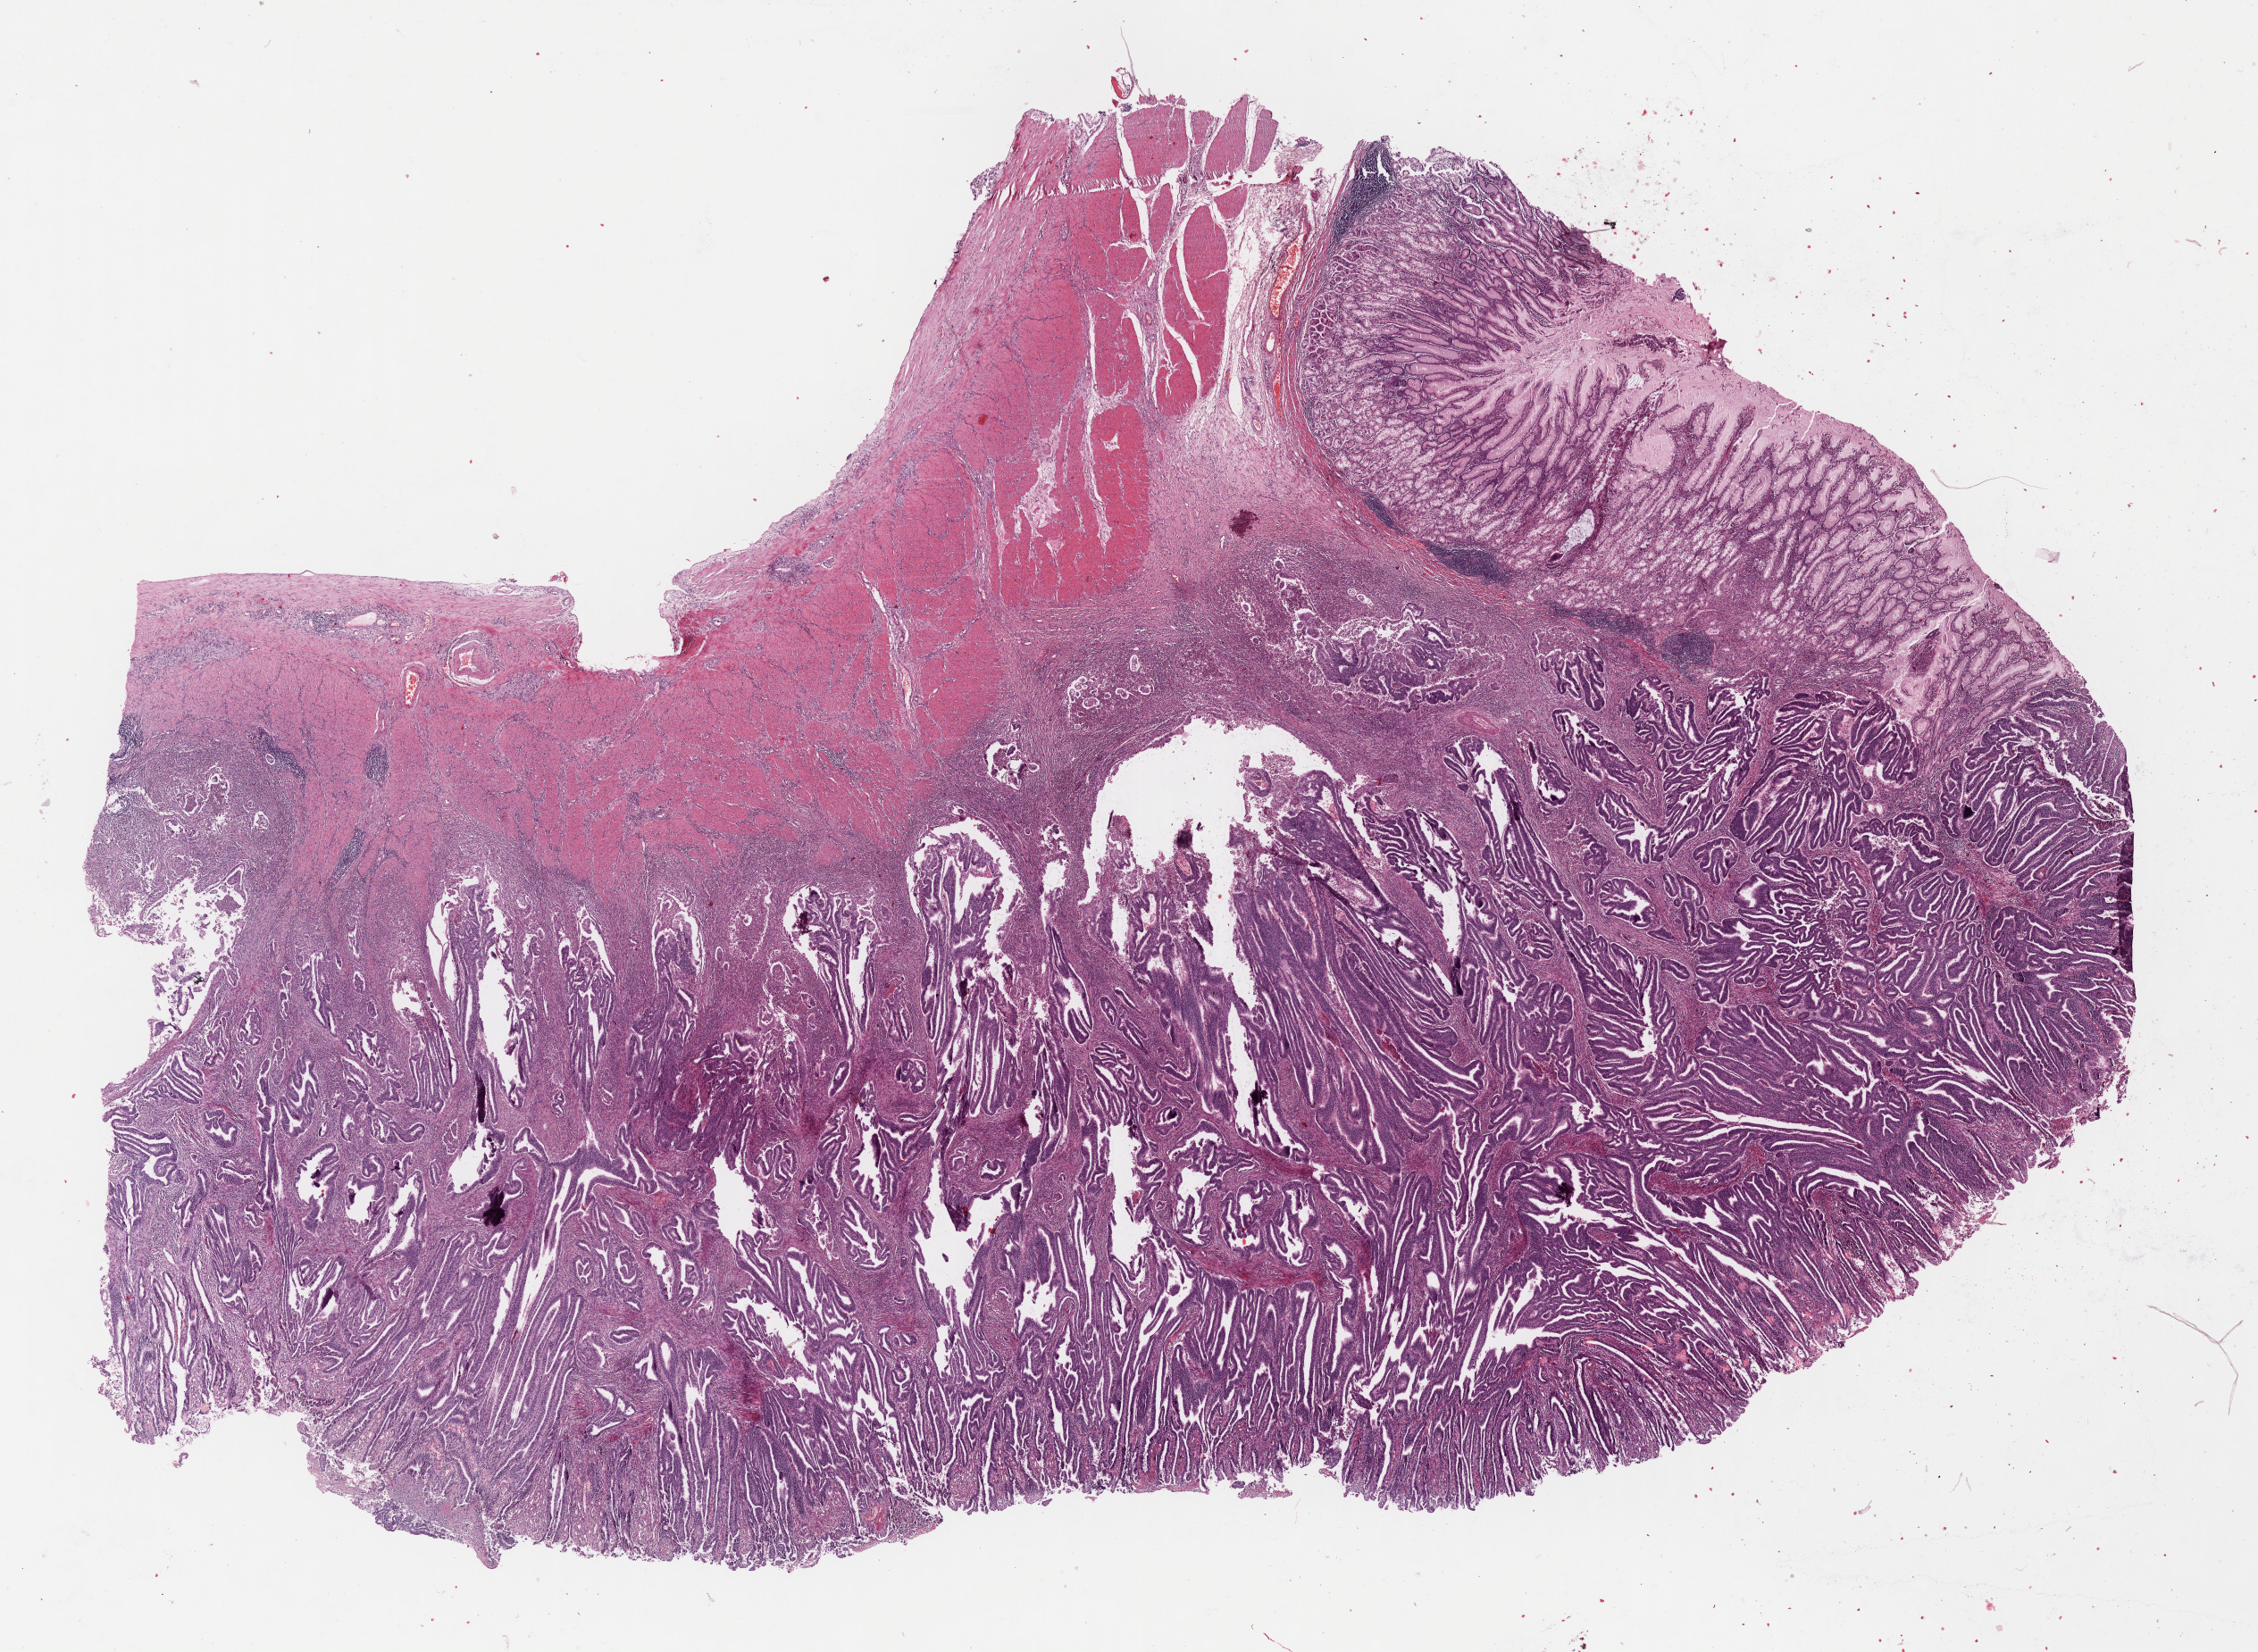
Digitized H&E-stained tissue section (whole slide) — whole scanned area (about 19.9 x 14.6 mm) shown as a low-resolution overview; formalin-fixed paraffin-embedded (FFPE) diagnostic section; primary tumour sample from the stomach. Male, age 57 years at initial diagnosis. Histologic grade: G2 (moderately differentiated).
- lymph nodes positive (case pathology): 6 of 10 examined
- AJCC pathologic stage: IIB
- diagnosis: Adenocarcinoma, NOS (fundus of stomach)